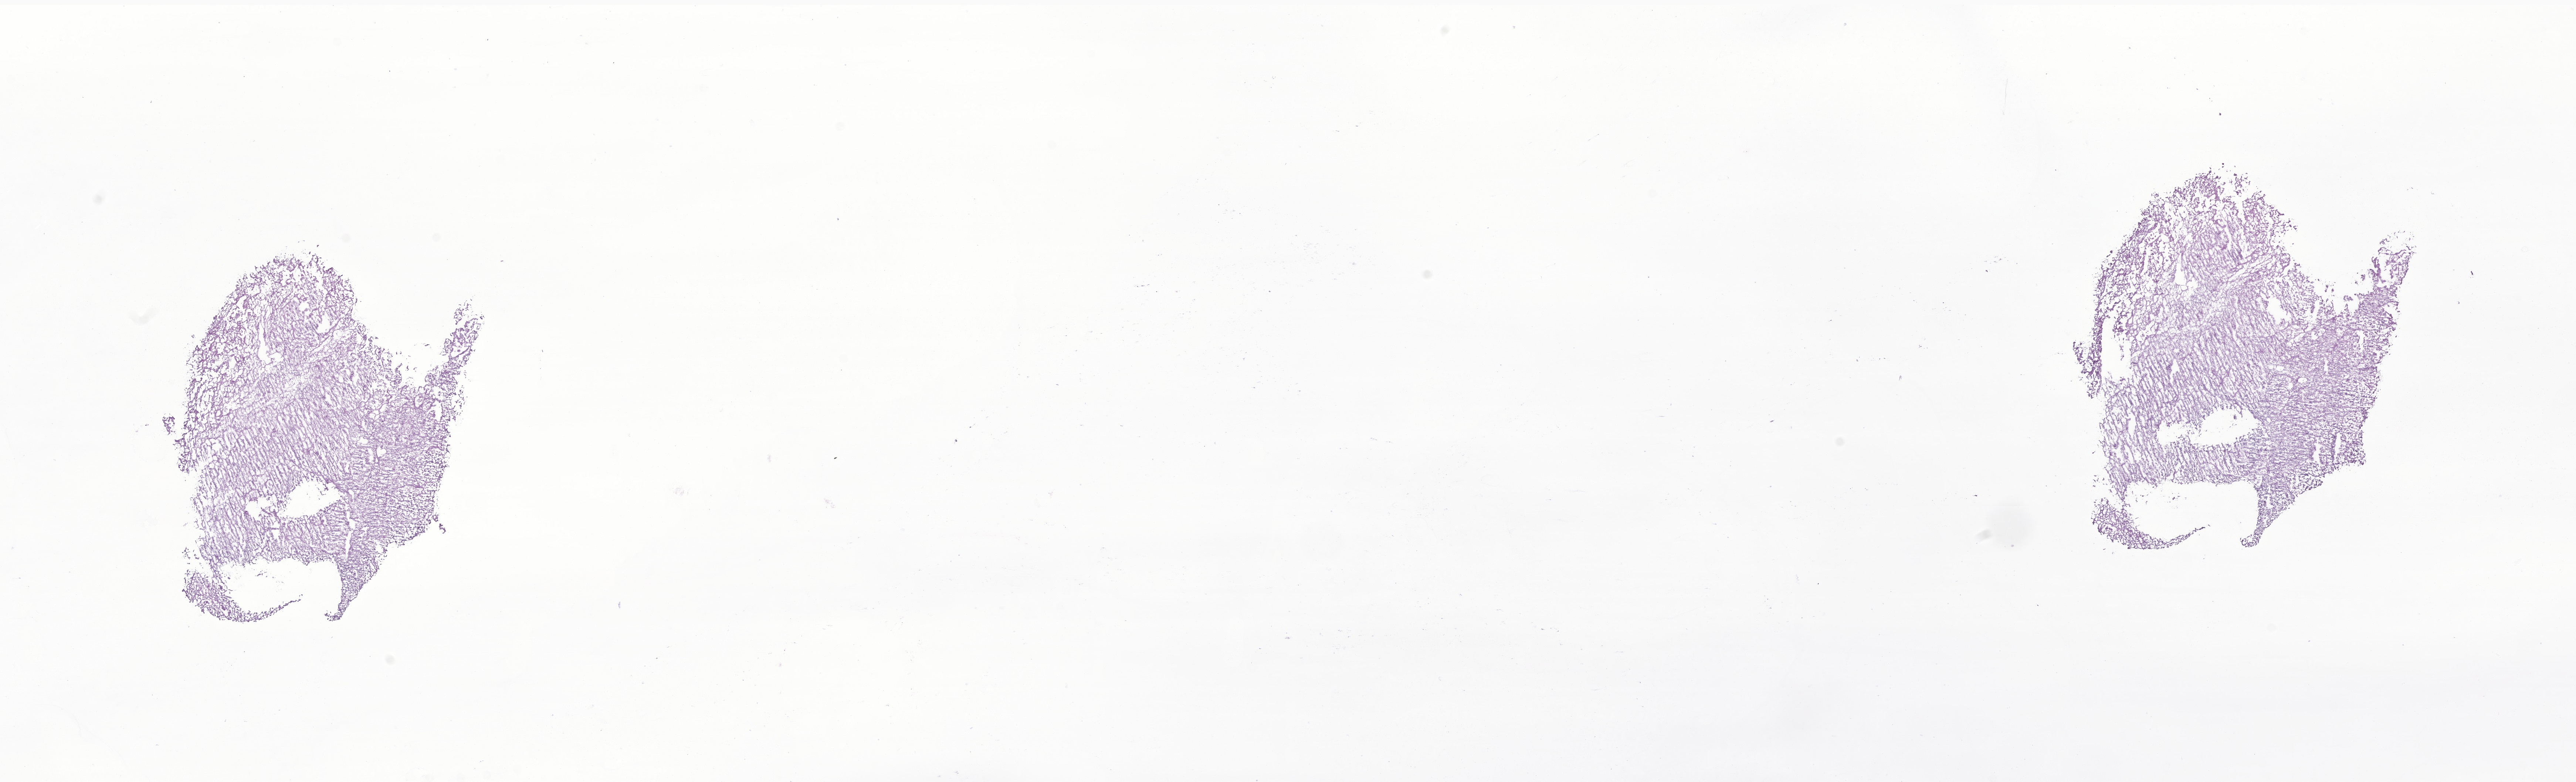
Whole-slide image, hematoxylin and eosin (H&E) stain of tumor tissue from the cerebellum — low-resolution overview of the scanned area, about 29.4 x 8.9 mm, frozen section. Patient: male, age 563 days (about 1.5 years).
Recorded diagnosis: Medulloblastoma, NOS.